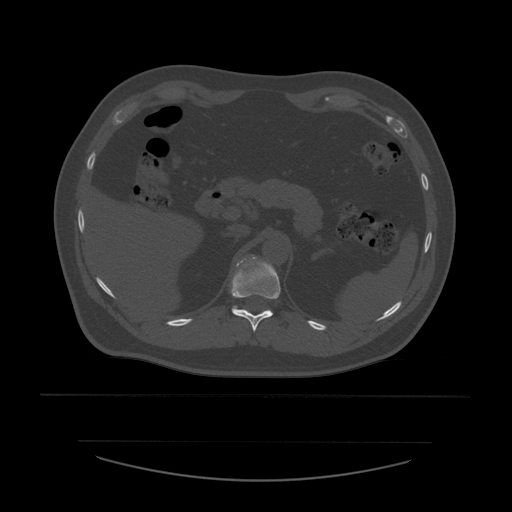
CT including the spine, one axial slice. Slice 270 of 532 in the series (ordered by position). Reconstruction kernel STANDARD. 120 kVp. Bone window (W 1800 / L 400 HU). 1.25 mm slice thickness. 512 × 512 image matrix, field of view 441 × 441 mm. Patient age 44 years. Case-level facts recorded for this patient, not image findings: primary cancer: soft tissue sarcoma.
Structures marked on this image (semi-automatic segmentation, software-assisted and operator-edited):
- T11 vertebra: bounding box [x1, y1, x2, y2] px = [231, 259, 281, 332]